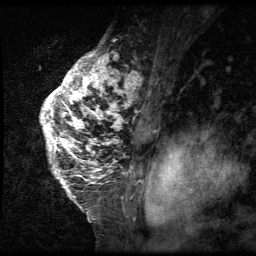
Breast MRI (dynamic contrast-enhanced), one sagittal slice. Slice 45 of 64 in the series (ordered by position). 3 images stored at this slice position (order not interpretable as contrast timing). 1.5 T. TE 4.2 ms, TR 9 ms. 2.5 mm slice thickness. 256 × 256 image matrix. Patient: female, 50 years. From the clinical record (not read from this slice): setting: breast cancer imaged before/during neoadjuvant chemotherapy; receptor status: triple-negative.
Structures marked on this image (semi-automatic segmentation, software-assisted and operator-edited):
- analysis volume of interest (the breast-tissue region the enhancement analysis was run in; not a lesion): box from (x=40, y=39) to (x=139, y=212) px
- tumour enhancement mask (voxels above the 140 % enhancement threshold inside the analysis volume of interest): (x=41, y=50)–(x=139, y=200)